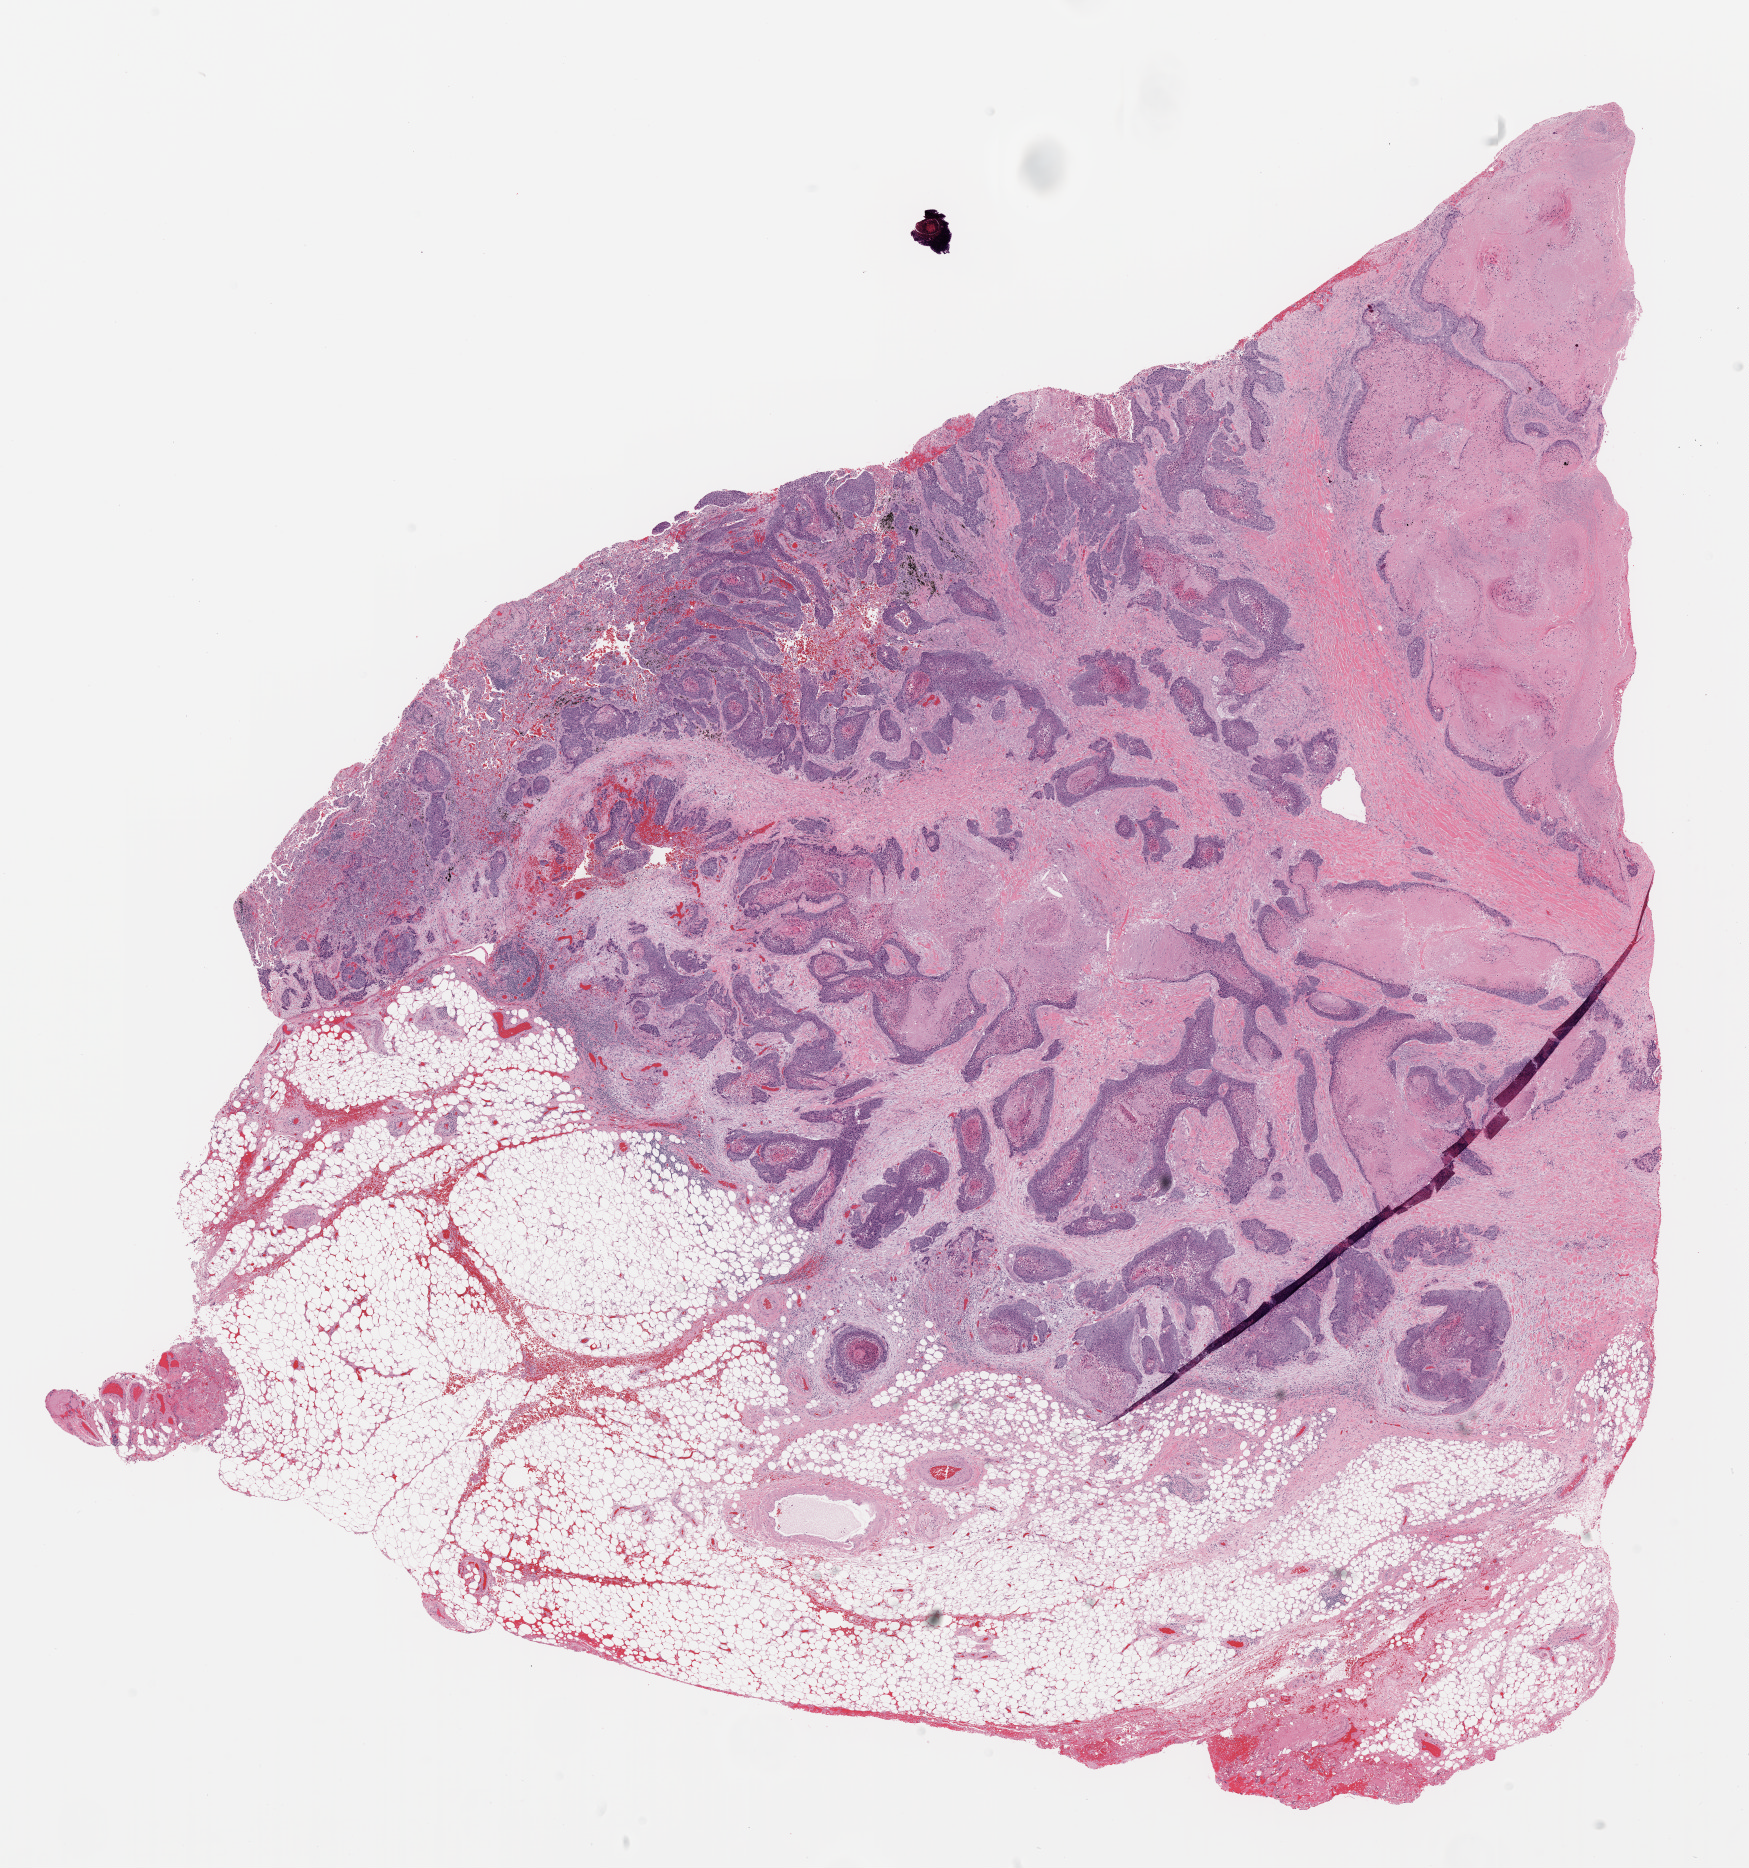
Digitized H&E tissue section (whole slide) — a low-resolution overview of the entire scanned area, about 14.0 x 15.0 mm (acquisition: 20x scan). Formalin-fixed paraffin-embedded (FFPE) diagnostic section. Sample: primary tumour, lung. Male patient.
AJCC pathologic stage: IIIA (6th edition). Diagnosis: Squamous cell carcinoma, NOS (upper lobe, lung).